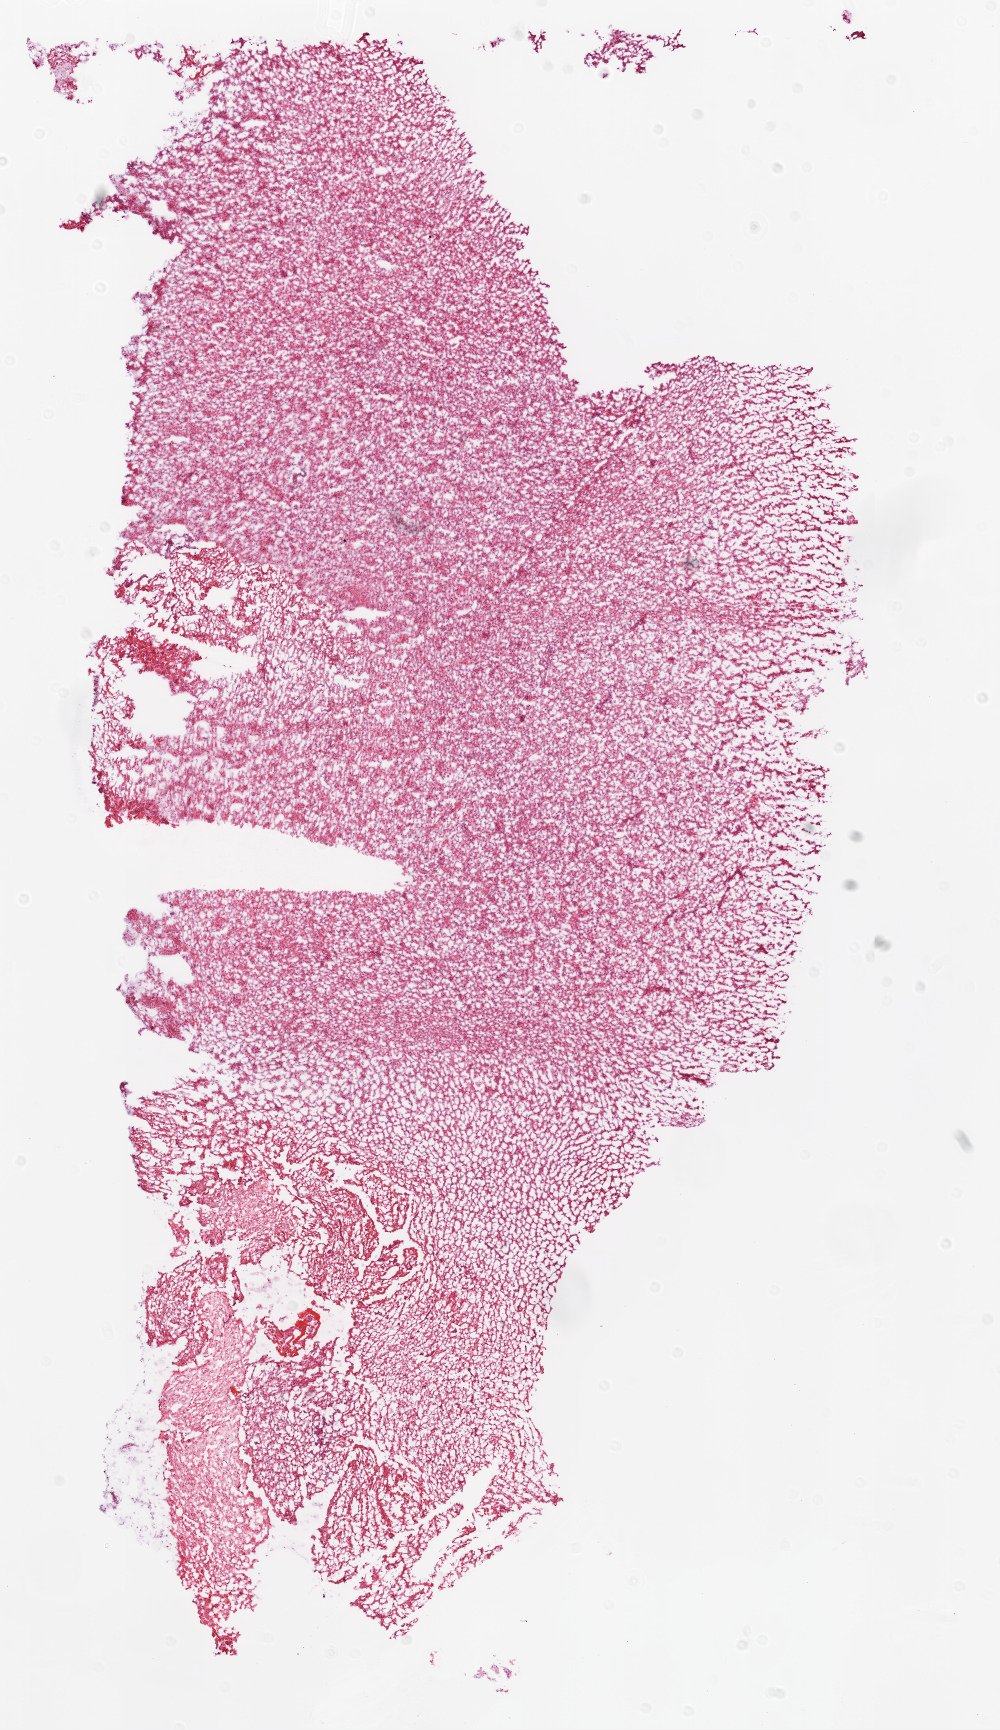
H&E whole-slide image, a low-resolution overview of the entire scanned area, about 8.0 x 13.9 mm. Frozen section. Sample: primary tumour, brain. Male, age 66 years at initial diagnosis. Slide review estimates, as recorded: tumour cells 90%, tumour nuclei 95%, normal cells 0%, stromal cells 5%, necrosis 5%.
• histologic diagnosis: Glioblastoma